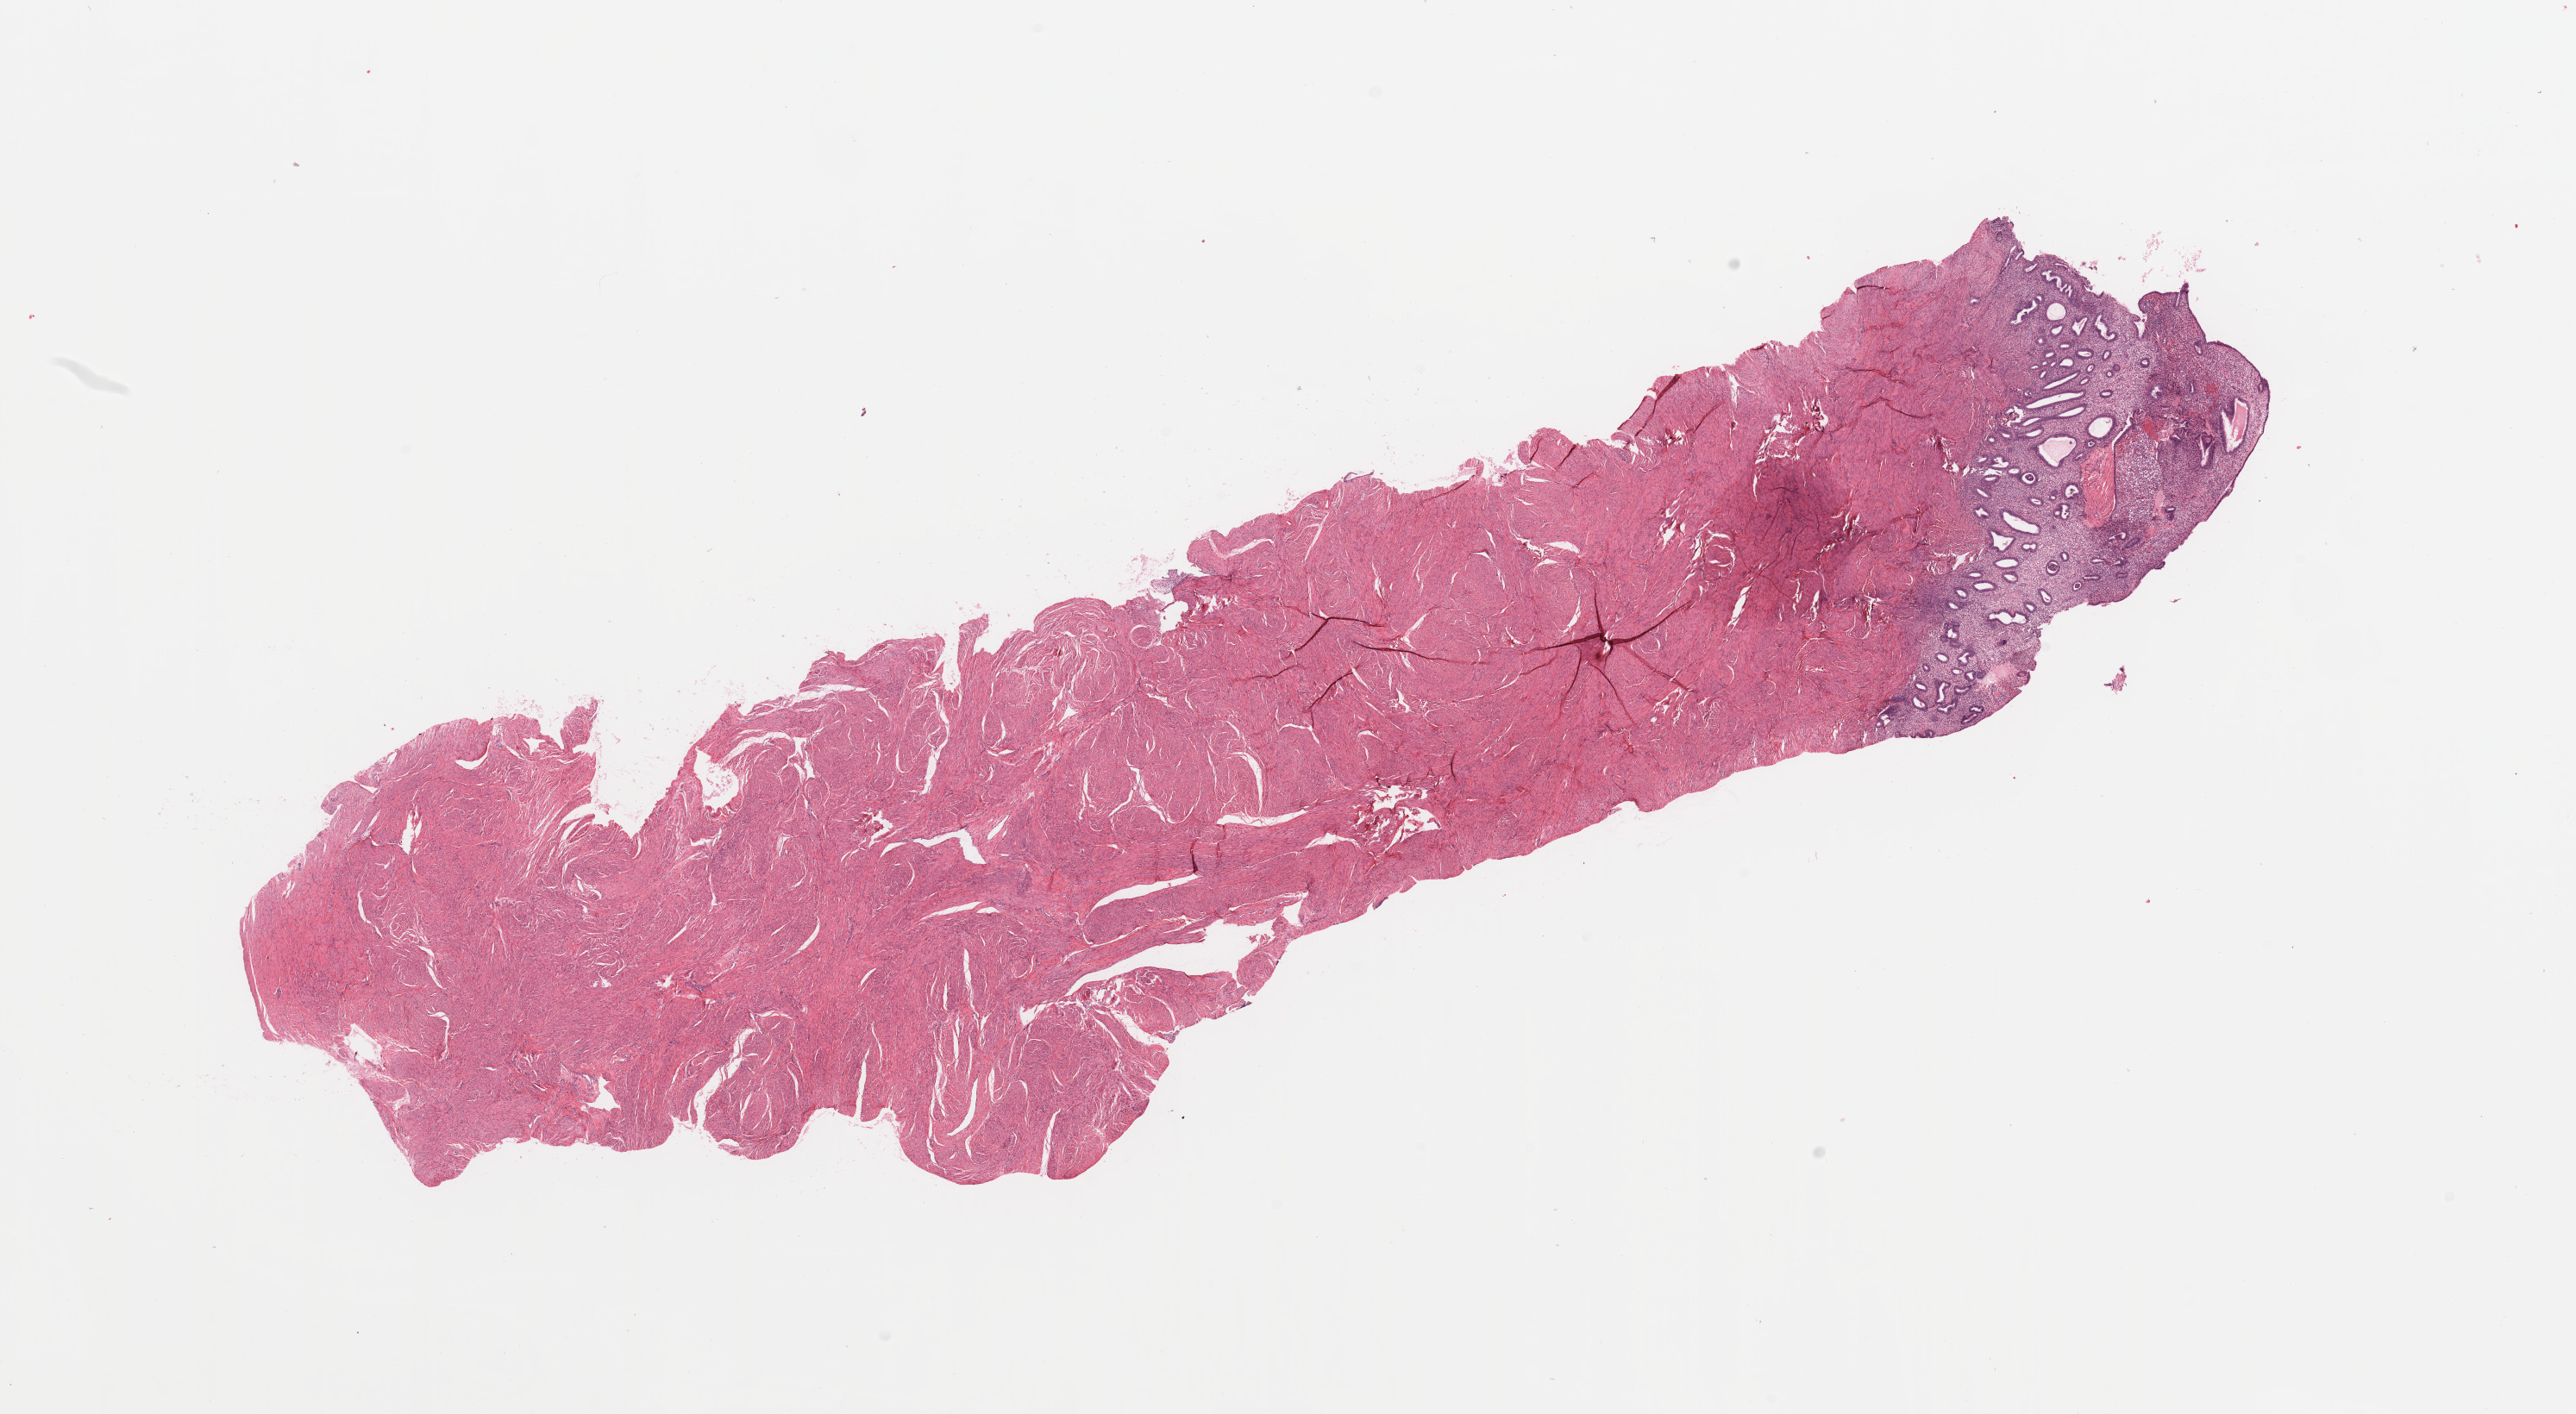
Digitized Hematoxylin and eosin (H&E) stained tissue section (whole slide), a low-resolution overview of the entire scanned area, about 23.6 x 13.0 mm (from a 20x scan). Normal (non-tumour) tissue sample, sampled site: uterus. Patient: female, age 51 years.
This section: normal (non-tumour) tissue from the same patient. Patient diagnosis: Endometrioid adenocarcinoma, NOS.